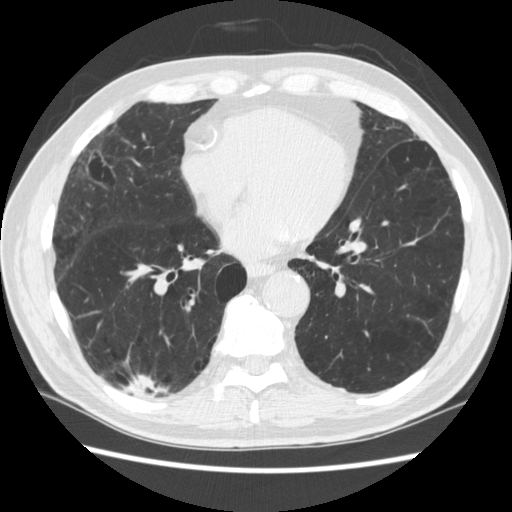
Low-dose screening chest CT, one axial slice; slice 111 of 266 in the series (ordered by position); reconstruction kernel STANDARD; 120 kVp; lung window (W 1500 / L -600 HU); 512 × 512 image matrix.
Outlined on this slice (expert manual segmentation):
- lesion 1 (tumor, upper lobe of right lung): box from (x=129, y=375) to (x=164, y=395) px